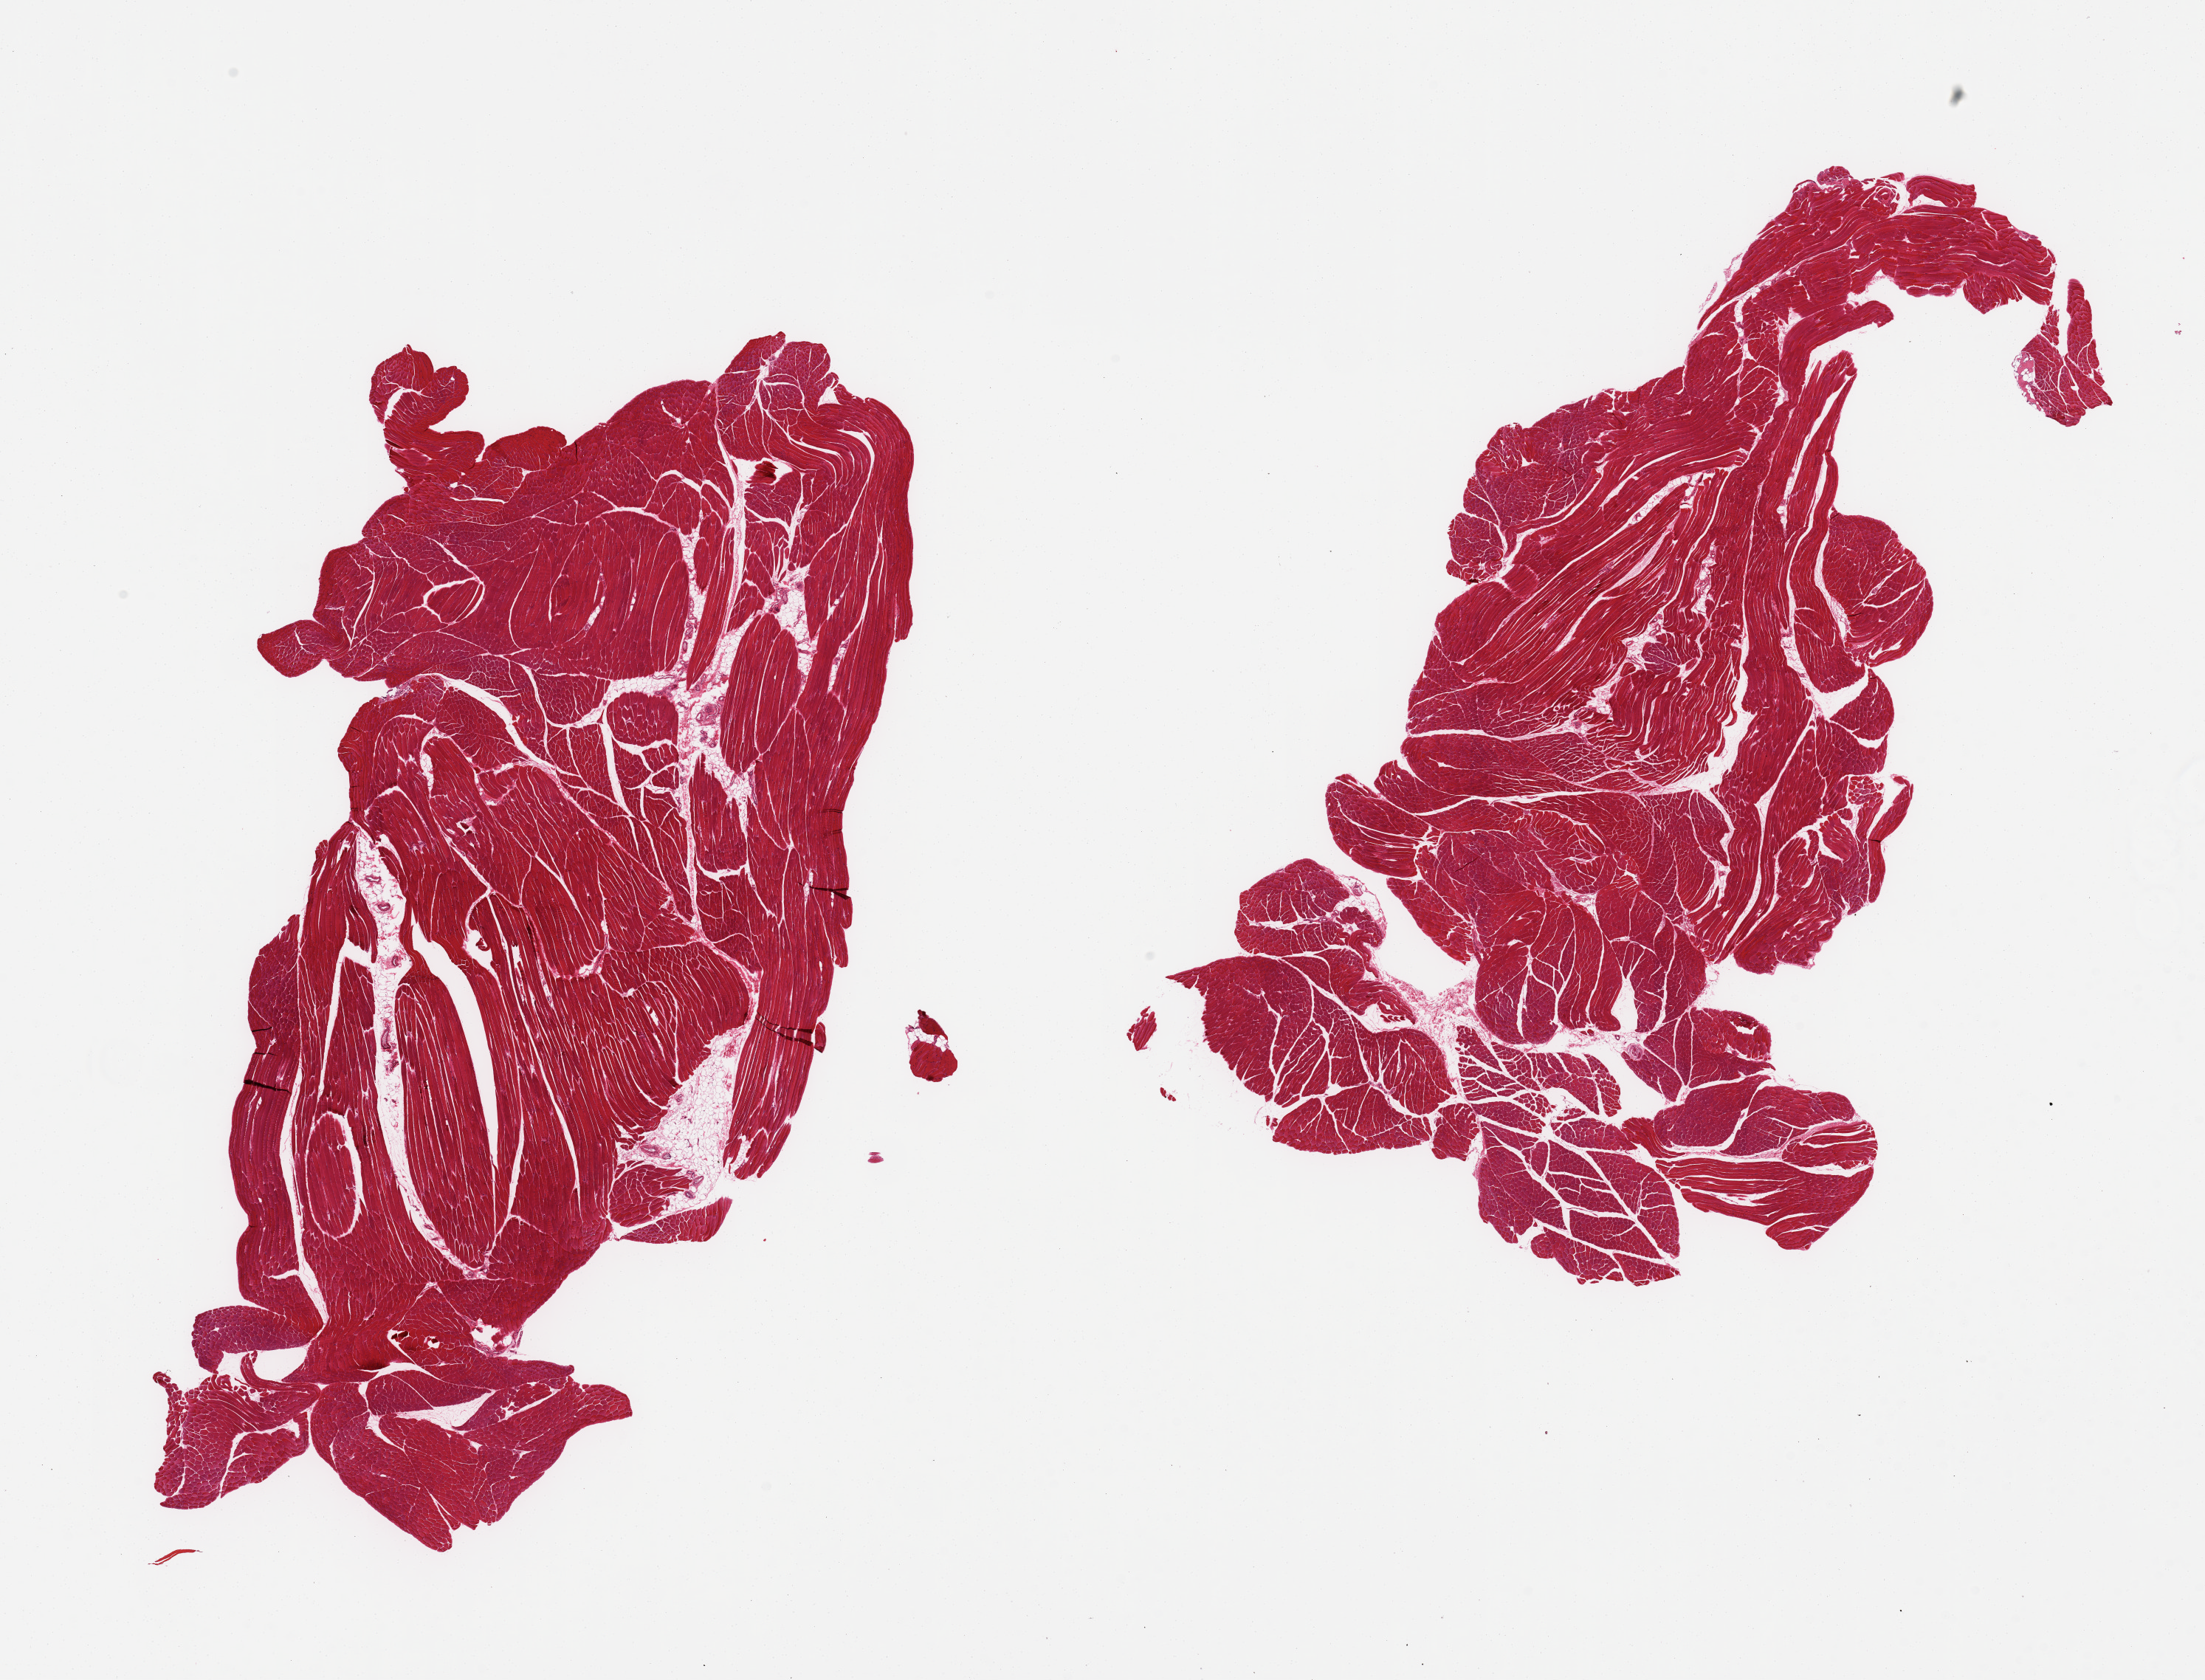
H&E whole-slide image, shown as a low-resolution overview of the whole scanned area (about 23.6 x 18.0 mm, from a 20x scan); PAXgene-fixed paraffin-embedded (PFPE) section; target tissue: skeletal muscle; tissue donor sample.
Reviewer comment on this tissue sample: 2 pieces, ~10% interstitial fat.